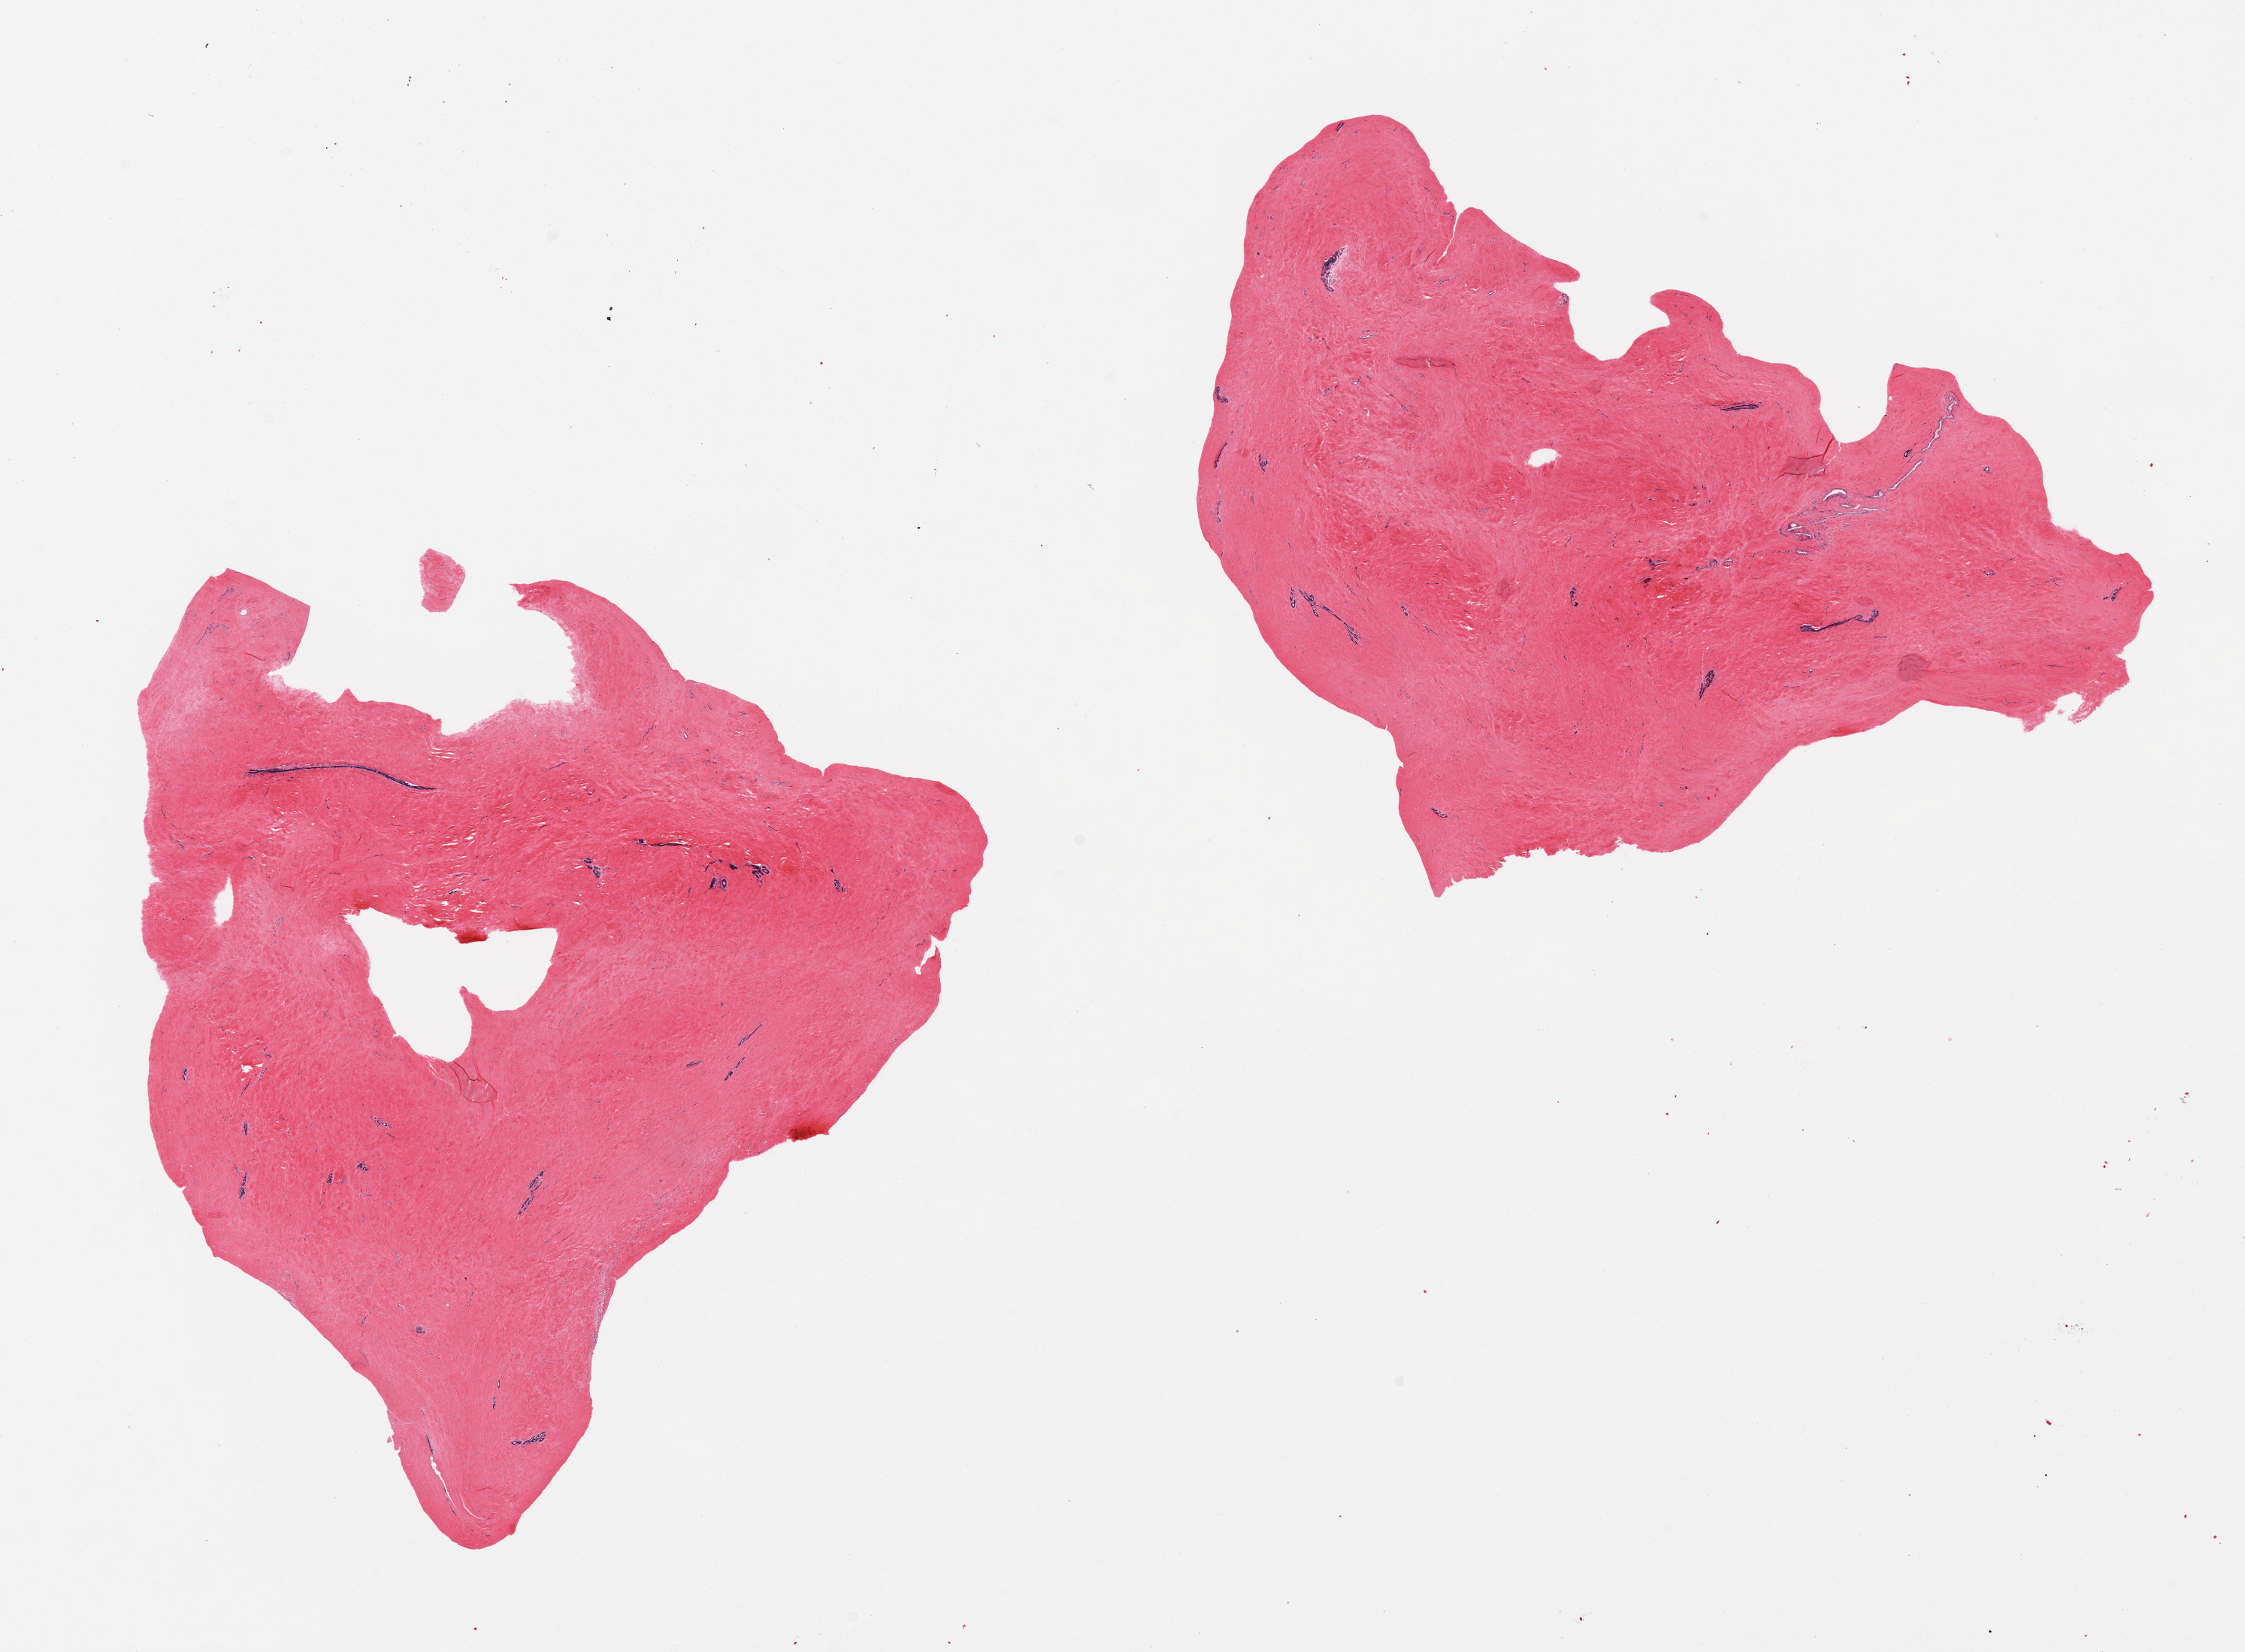
Digitized haematoxylin and eosin-stained section, brightfield, whole scanned area (about 23.6 x 17.4 mm) shown as a low-resolution overview. PAXgene-fixed, paraffin-embedded tissue. Target tissue: breast. Donor tissue sample. Donor: male.
Reviewer comment on this tissue sample: 2 pieces, dense stromal fibrosis, atrophic ductal elements visible.